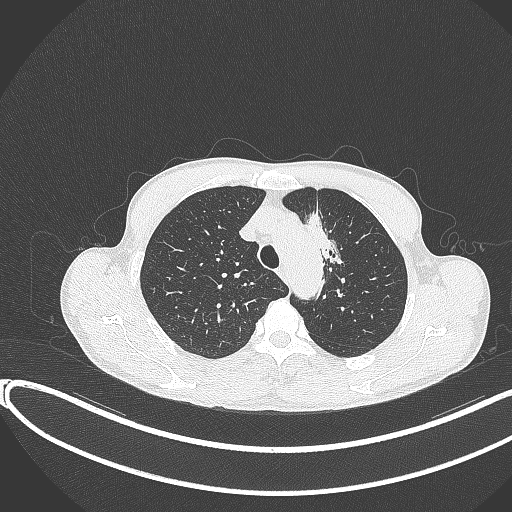
Chest CT, one axial slice. Slice 296 of 374 in the series (ordered by position). 120 kVp. Lung window (W 1500 / L -600 HU). 1 mm slice thickness. 512 × 512 image matrix, field of view 400 × 400 mm. Male patient, age 58 years. Case-level facts recorded for this patient, not image findings: clinical TNM (as recorded): T1c N1 M0.
Outlined on this slice (rectangle marked by the reading radiologist):
- lung tumour (recorded histology: adenocarcinoma): bounding box (x1, y1, x2, y2) in pixels: (301, 207, 345, 277)